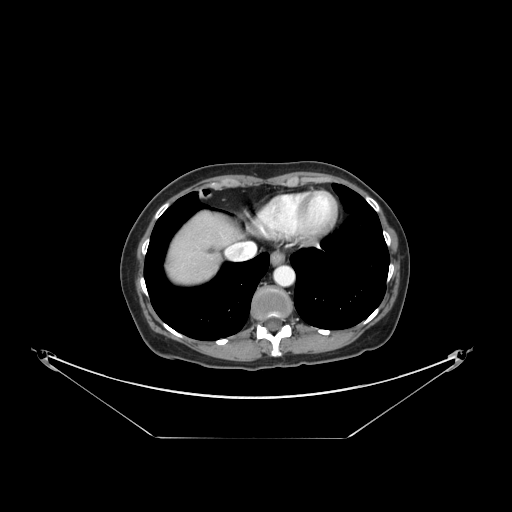
Contrast-enhanced abdominal CT, one axial slice; position 134 of 148 along the scan axis; reconstruction kernel STANDARD; intravenous contrast given; soft-tissue window (W 400 / L 40 HU); 512 × 512 image matrix. Female patient, age 73 years. From the clinical record (not read from this slice): diagnosis: colorectal cancer liver metastases, imaged before liver resection; multiple liver metastases: no; largest metastasis: 1 cm.
Structures marked on this image (outlined manually by an expert reader):
- liver: bounding box [x1, y1, x2, y2] px = [167, 215, 238, 284]
- planned liver remnant (the part of the liver to remain after resection): [199, 215, 236, 240]
- liver metastasis: [207, 247, 217, 257]